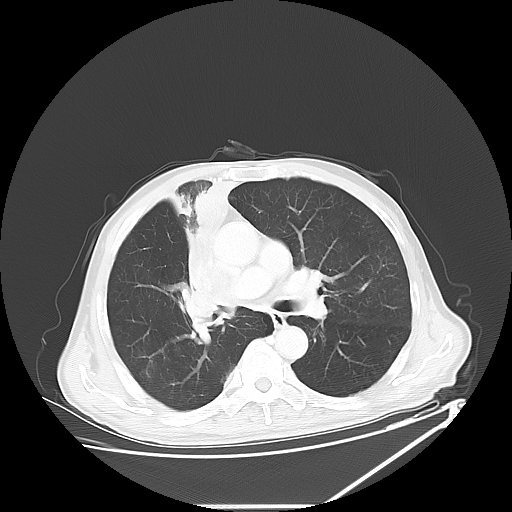
Chest CT, one axial slice. Slice 37 of 60 in the series (ordered by position). Reconstruction kernel LUNG. Lung window (W 1500 / L -600 HU). 5 mm slice thickness. 512 × 512 image matrix. Patient: male, 73 years. From the clinical record (not read from this slice): clinical TNM (as recorded): T2a N1 M0.
Annotated regions visible in this slice (bounding box drawn by a radiologist):
- lung tumour (recorded histology: squamous cell carcinoma): bounding box [x1, y1, x2, y2] px = [177, 178, 231, 339]